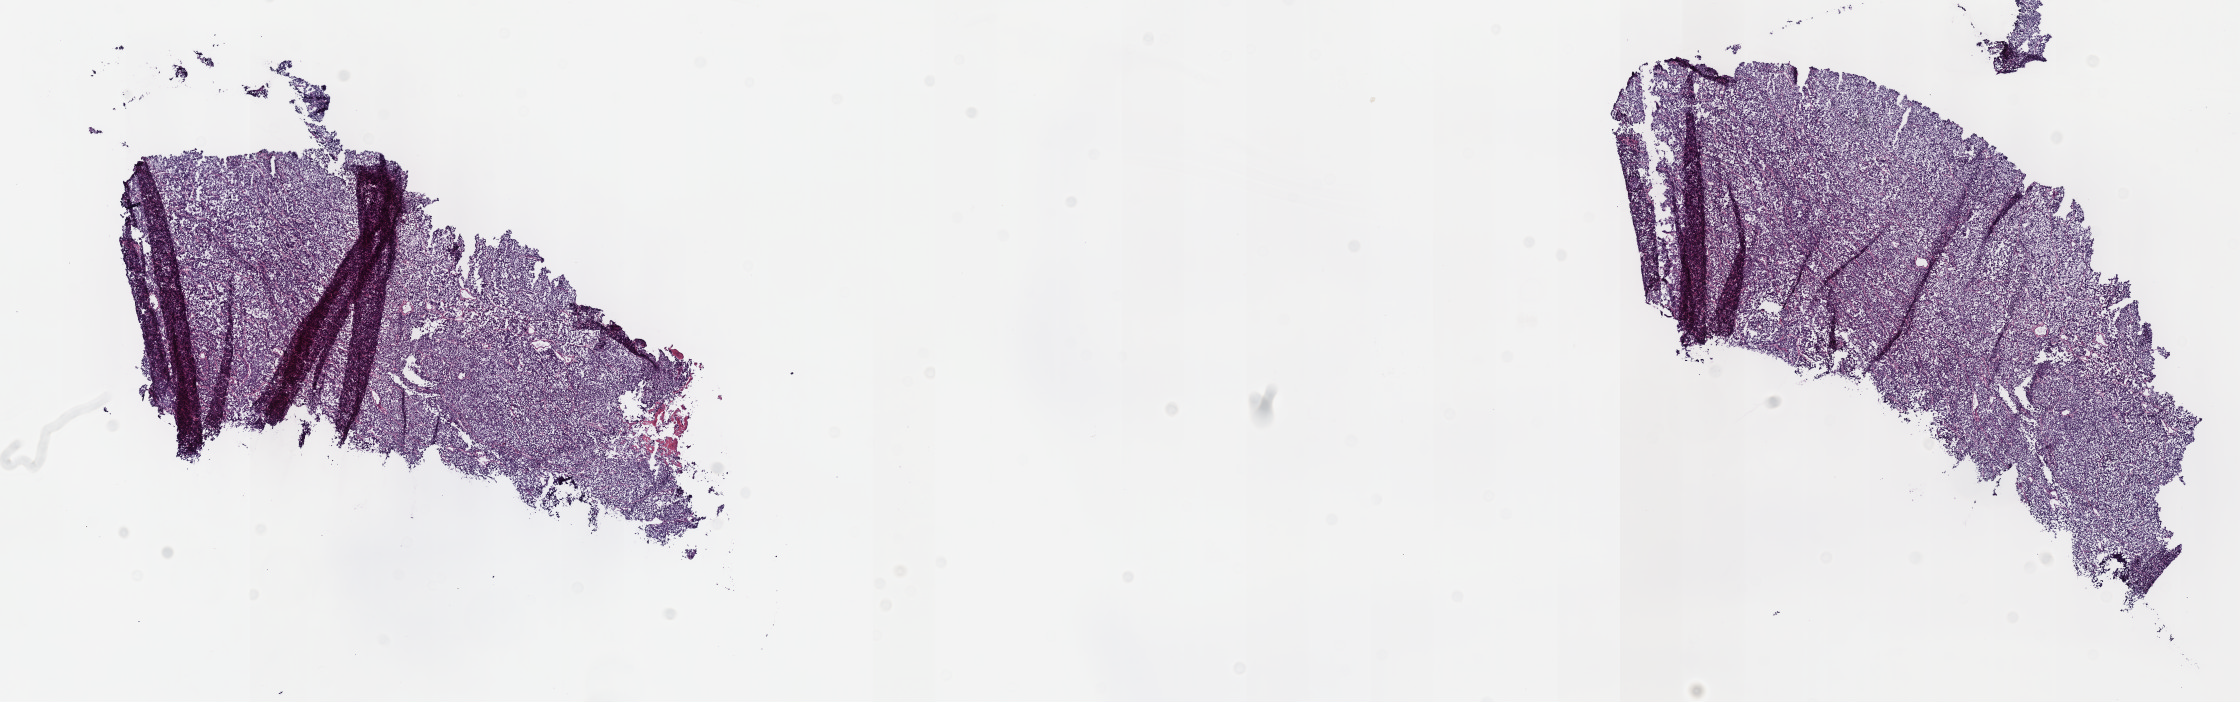
H&E whole-slide image — low-resolution overview of the scanned area, about 18.1 x 5.7 mm (from a 40x scan). Frozen section from the top of the tissue portion. Primary tumour sample from the cervix. Female, age 35 years at initial diagnosis. Histologic grade: G3 (poorly differentiated). Pathologist review of this section (percent, as recorded): tumour cells 80%, tumour nuclei 80%, normal cells 0%, stromal cells 10%, necrosis 10%. Inflammatory infiltration, as recorded: lymphocyte infiltration 40%, monocyte infiltration 20%, neutrophil infiltration 20%.
- pathologic diagnosis: Squamous cell carcinoma, NOS (cervix uteri)
- FIGO stage: IB2